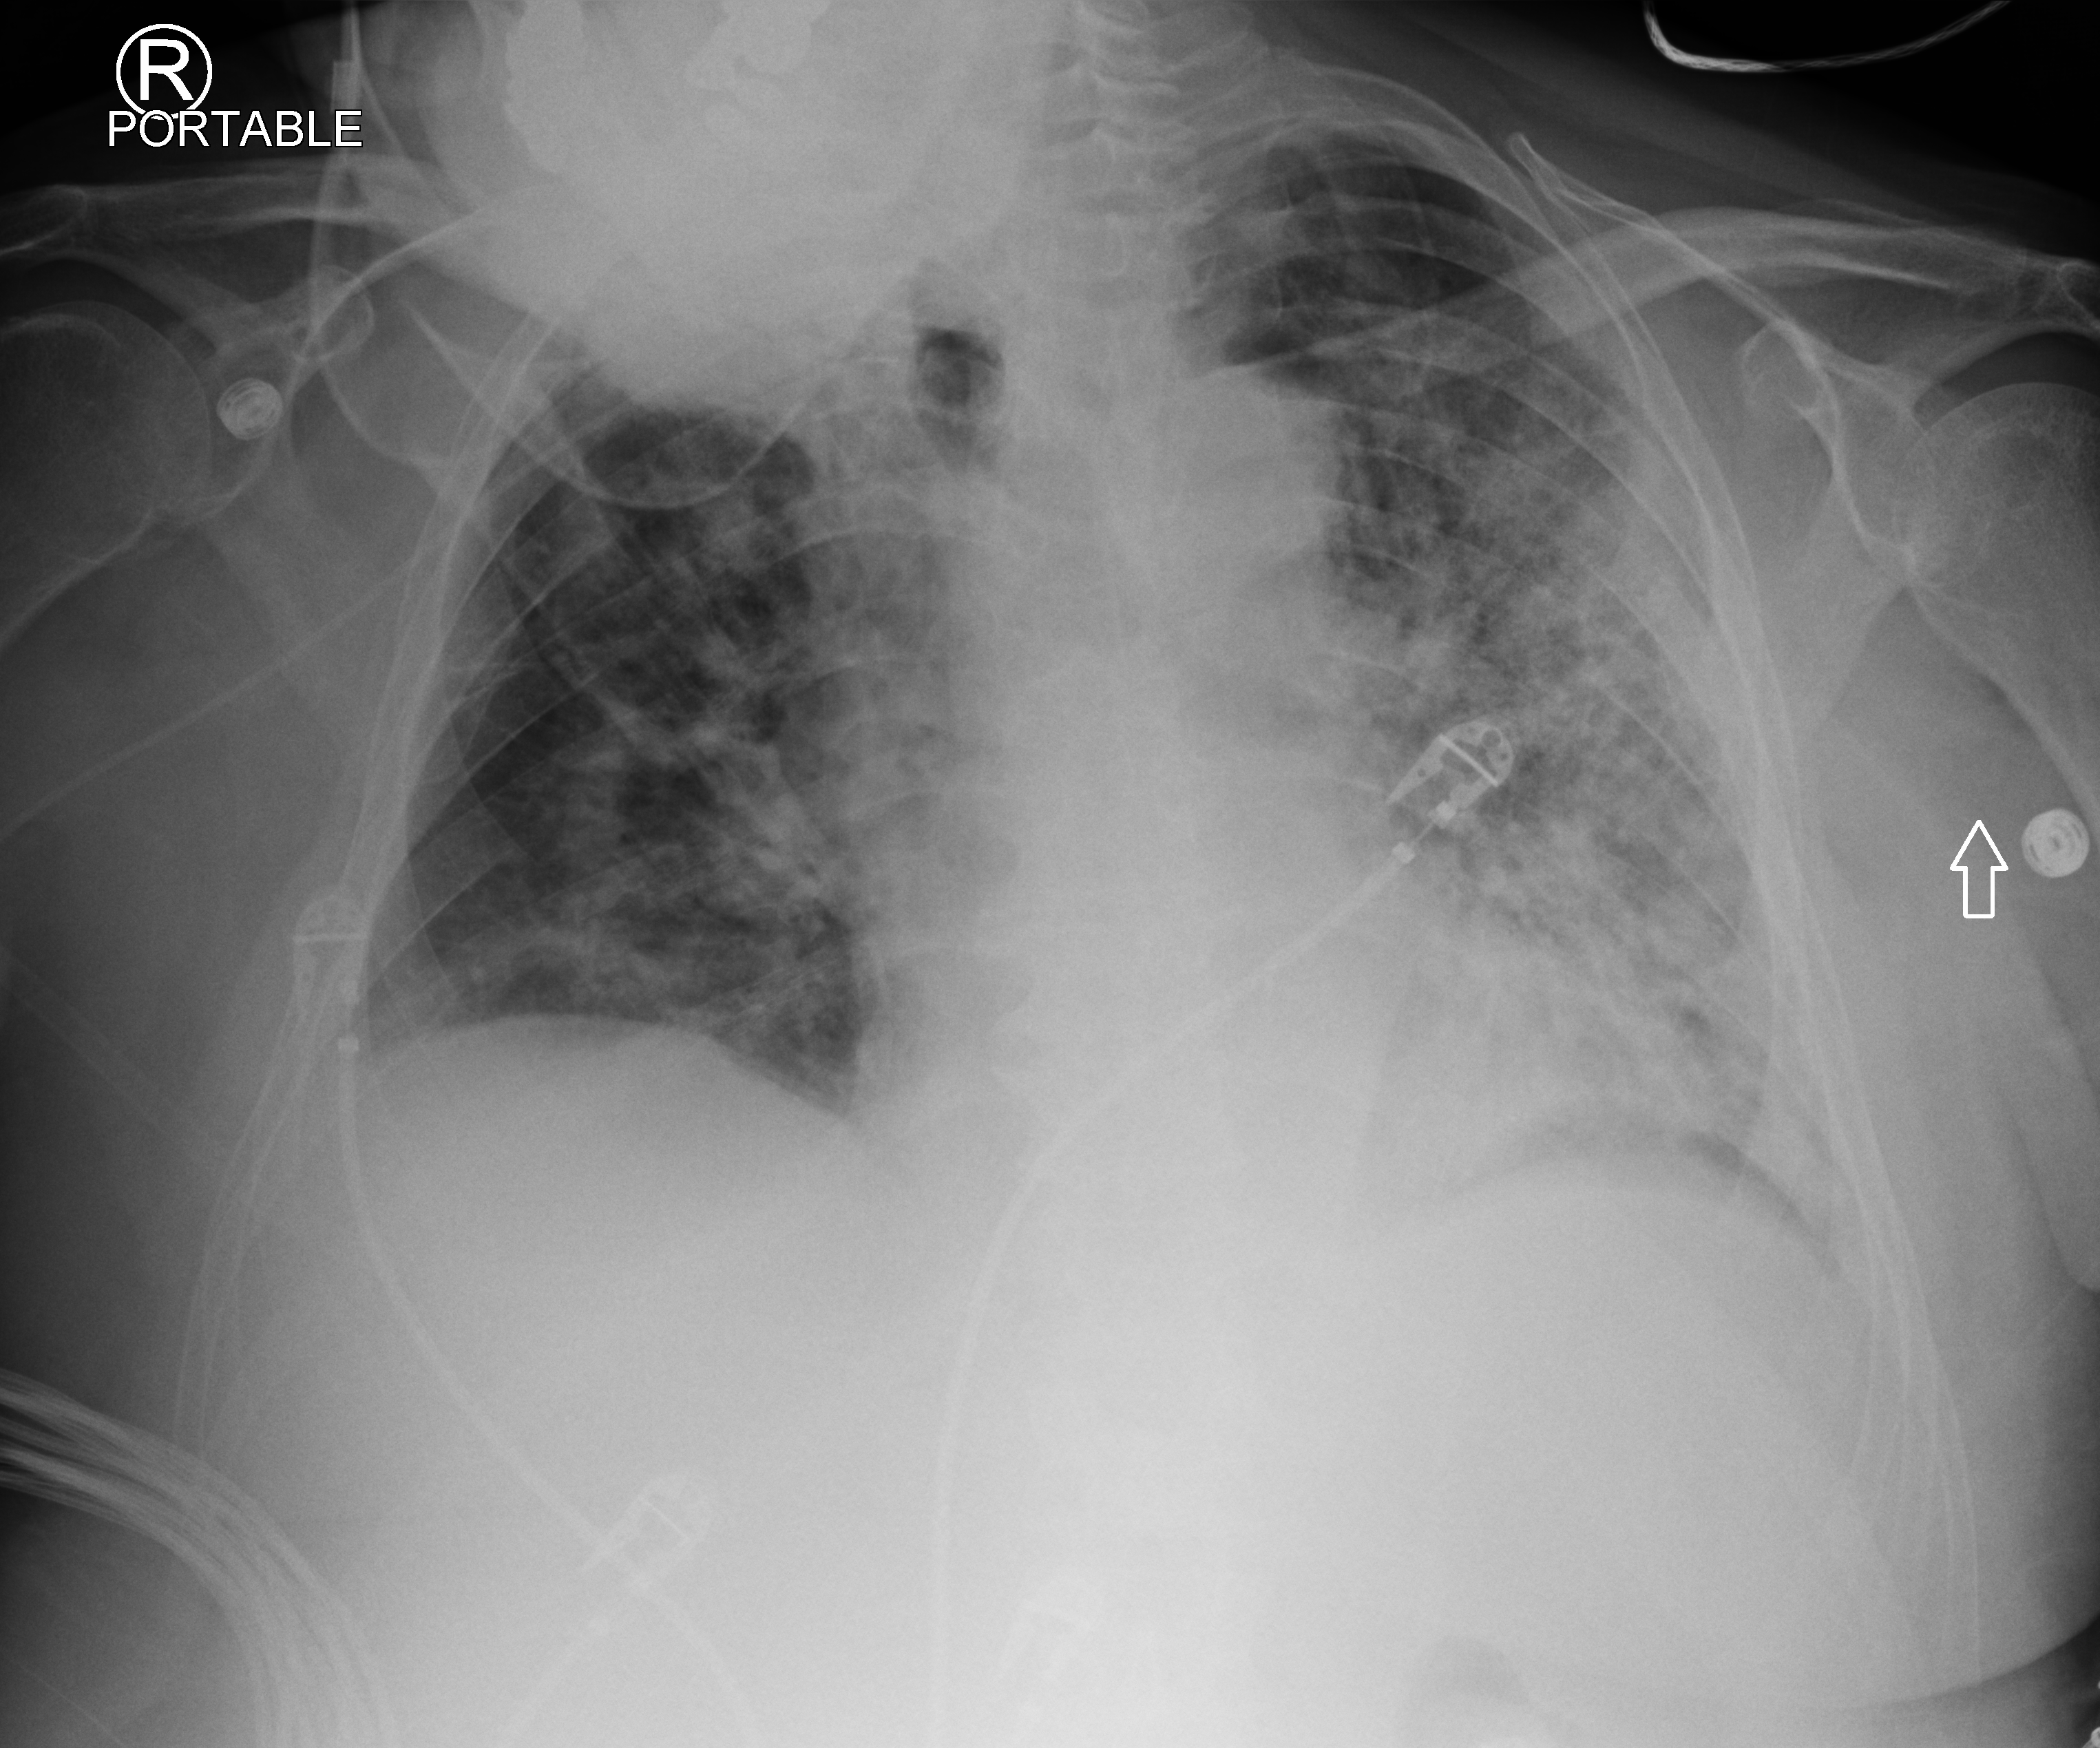
Chest X-ray (portable), anteroposterior (AP) projection. Male patient hospitalised with COVID-19, age 60–74 years.
Hospital-stay facts (about this admission, not read from this image; timing relative to this image not recorded):
- other chronic lung disease (admission record): no
- smoking status (admission record): never
- admitted to intensive care during this hospital stay: yes